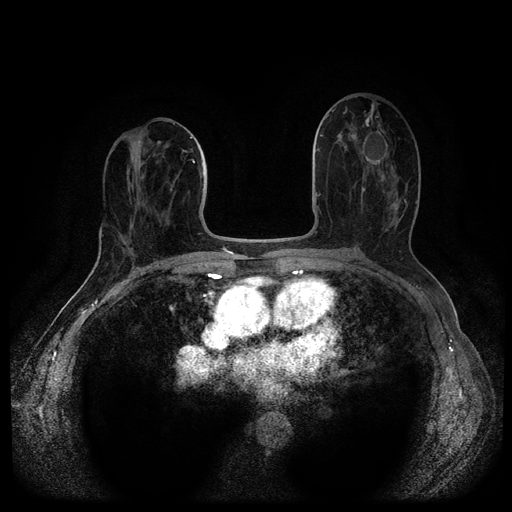
Breast MRI (dynamic contrast-enhanced, multi-phase), one axial slice; slice 52 of 116 in the series (ordered by position); dynamic contrast-enhanced series, time point 2 of 5 at this slice position (early post-contrast); 1.5 T; TE 2.6 ms, TR 5.4 ms; 2.1 mm slice thickness; 512 × 512 image matrix, field of view 340 × 340 mm. Female patient, age 69 years.
Outlined on this slice (semi-automatic segmentation, software-assisted and operator-edited):
- breast lesion (labelled benign in the annotation): box from (x=362, y=131) to (x=388, y=167) px